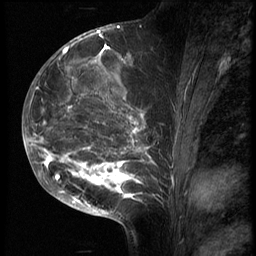
Breast MRI (dynamic contrast-enhanced), one sagittal slice. Position 31 of 70 along the scan axis. 3 images stored at this slice position (order not interpretable as contrast timing). 1.5 T. TE 4.2 ms, TR 9 ms. 2.5 mm slice thickness. 256 × 256 image matrix, field of view 180 × 180 mm. Patient: female, 28 years. Case-level facts recorded for this patient, not image findings: setting: breast cancer imaged before/during neoadjuvant chemotherapy.
Annotated regions visible in this slice (semi-automatically segmented with operator editing):
- analysis volume of interest (the breast-tissue region the enhancement analysis was run in; not a lesion): bounding box [x1, y1, x2, y2] px = [43, 42, 173, 215]
- tumour enhancement mask (voxels above the 140 % enhancement threshold inside the analysis volume of interest): [43, 47, 156, 203]